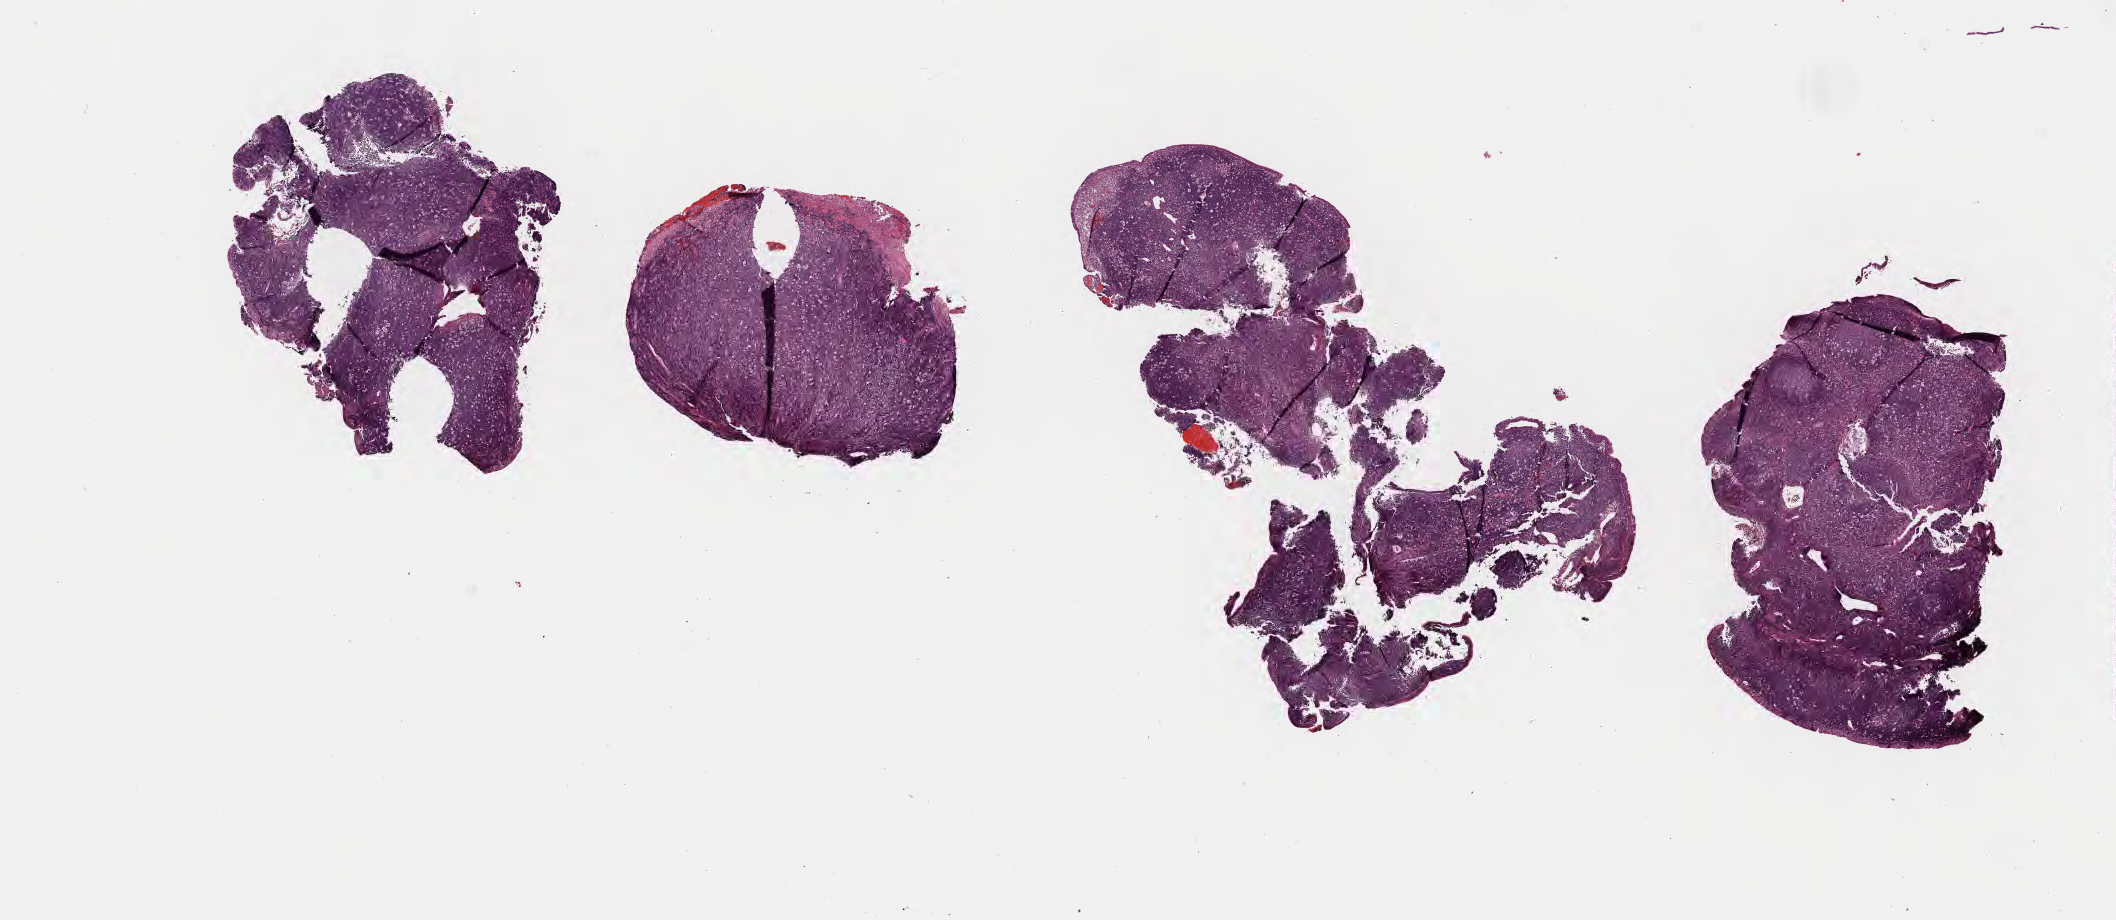
Digitized H&E-stained section — shown as a low-resolution overview of the whole scanned area (about 17.1 x 7.4 mm), FFPE section, specimen: primary tumor. Male, age 5 years at initial diagnosis. Slide review estimates, as recorded: tumor cells 70%, tumor nuclei 70%.
Histologic diagnosis: Burkitt lymphoma, NOS.